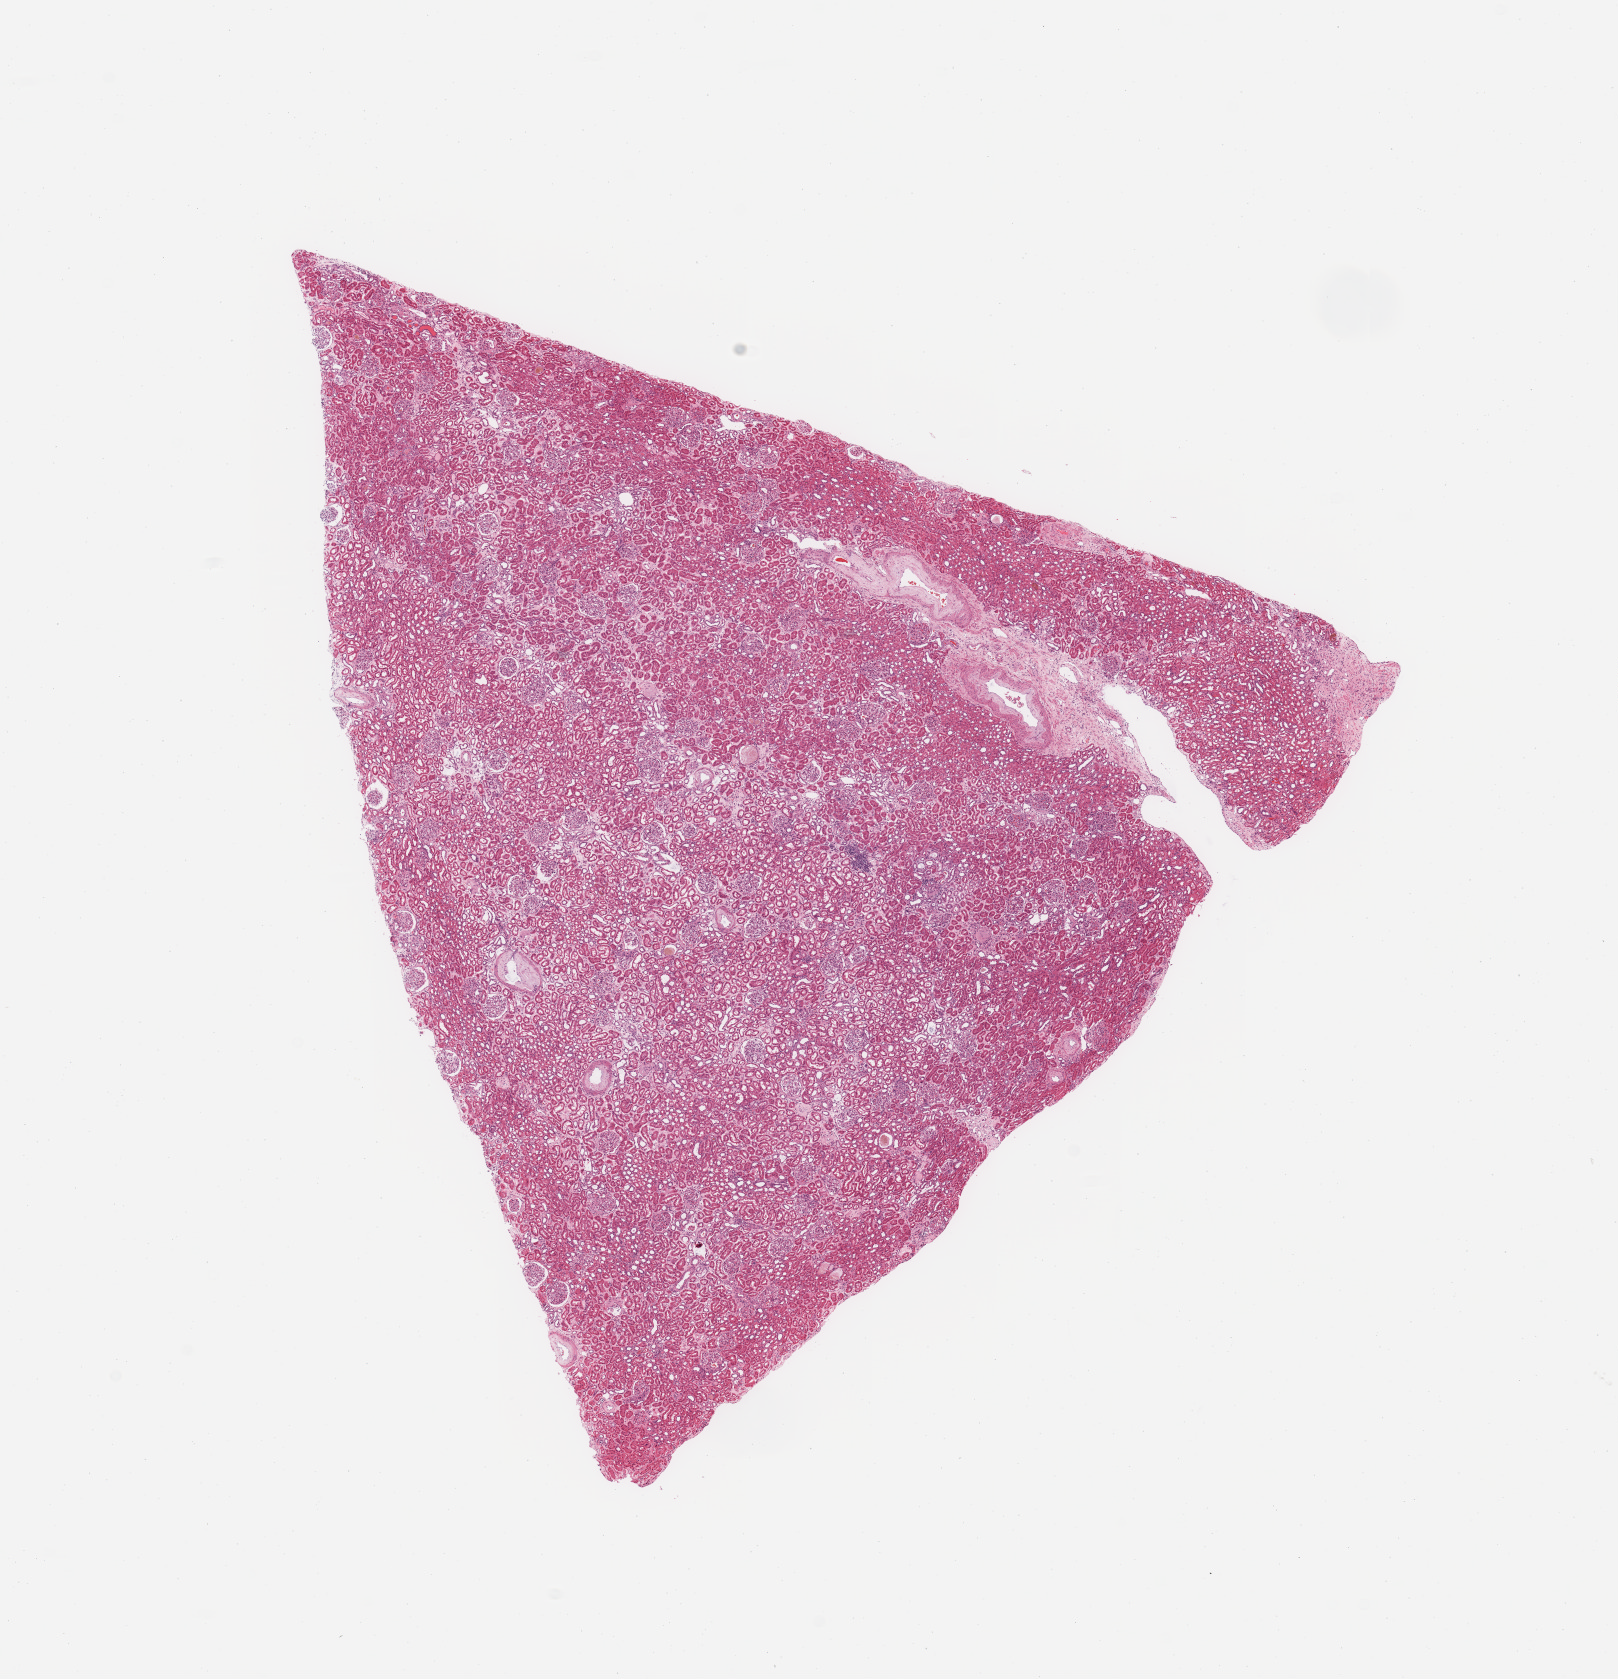
Digitized H&E-stained tissue section (whole slide) — whole scanned area (about 12.8 x 13.3 mm, slide scanned at 20x) shown as a low-resolution overview. Patient: male, age 68 years.
* patient diagnosis (cohort enrolment): sarcoma (site not recorded at cohort level)